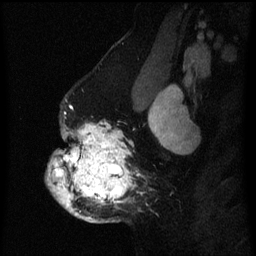
Breast MRI (dynamic contrast-enhanced), one sagittal slice; slice 45 of 60 in the series (ordered by position); dynamic contrast-enhanced series, image 2 of 3 at this slice position (ordered by acquisition); 1.5 T; TE 4.2 ms, TR 8 ms; 2 mm slice thickness; 256 × 256 image matrix, field of view 190 × 190 mm. Female patient, age 50 years.
Outlined on this slice (semi-automatic segmentation, software-assisted and operator-edited):
- analysis volume of interest (the breast-tissue region the enhancement analysis was run in; not a lesion): box from (x=45, y=116) to (x=154, y=223) px
- tumour enhancement mask (voxels above the 70 % enhancement threshold inside the analysis volume of interest): (x=48, y=122)–(x=135, y=219)